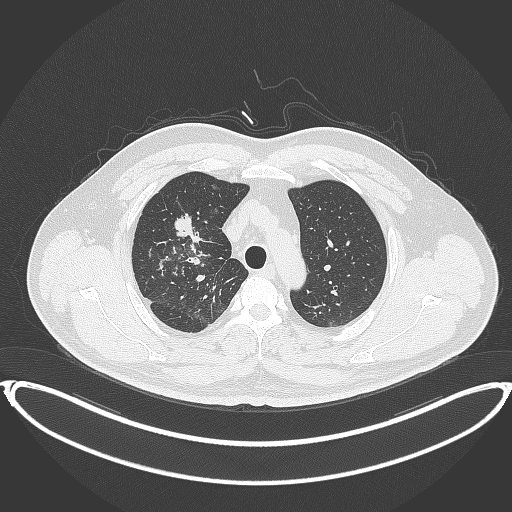
Chest CT, one axial slice; slice 299 of 399 in the series (ordered by position); reconstruction kernel B70f; 120 kVp; lung window (W 1500 / L -600 HU); 1 mm slice thickness; 512 × 512 image matrix, field of view 445 × 445 mm. Male patient, age 53 years. From the clinical record (not read from this slice): clinical TNM (as recorded): T2a N0 M0.
Outlined on this slice (rectangle marked by the reading radiologist):
- lung tumour (recorded histology: adenocarcinoma): box from (x=171, y=211) to (x=199, y=240) px